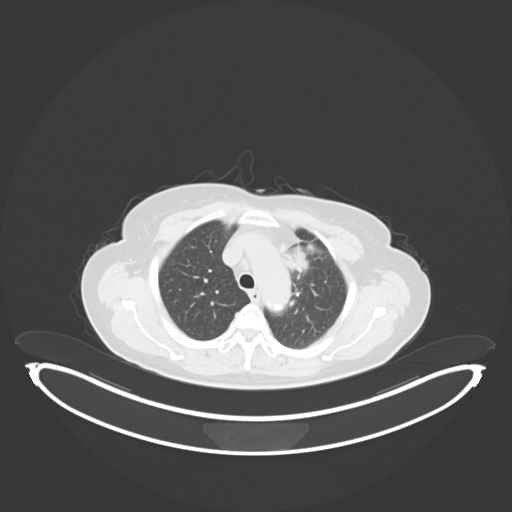
Chest CT, one axial slice. Position 196 of 243 along the scan axis. 120 kVp. Lung window (W 1500 / L -600 HU). 3 mm slice thickness. 512 × 512 image matrix. Female patient, age 65 years. From the clinical record (not read from this slice): clinical TNM (as recorded): T2a N0 M0.
Outlined on this slice (rectangle marked by the reading radiologist):
- lung tumour (recorded histology: adenocarcinoma): box from (x=279, y=241) to (x=319, y=273) px